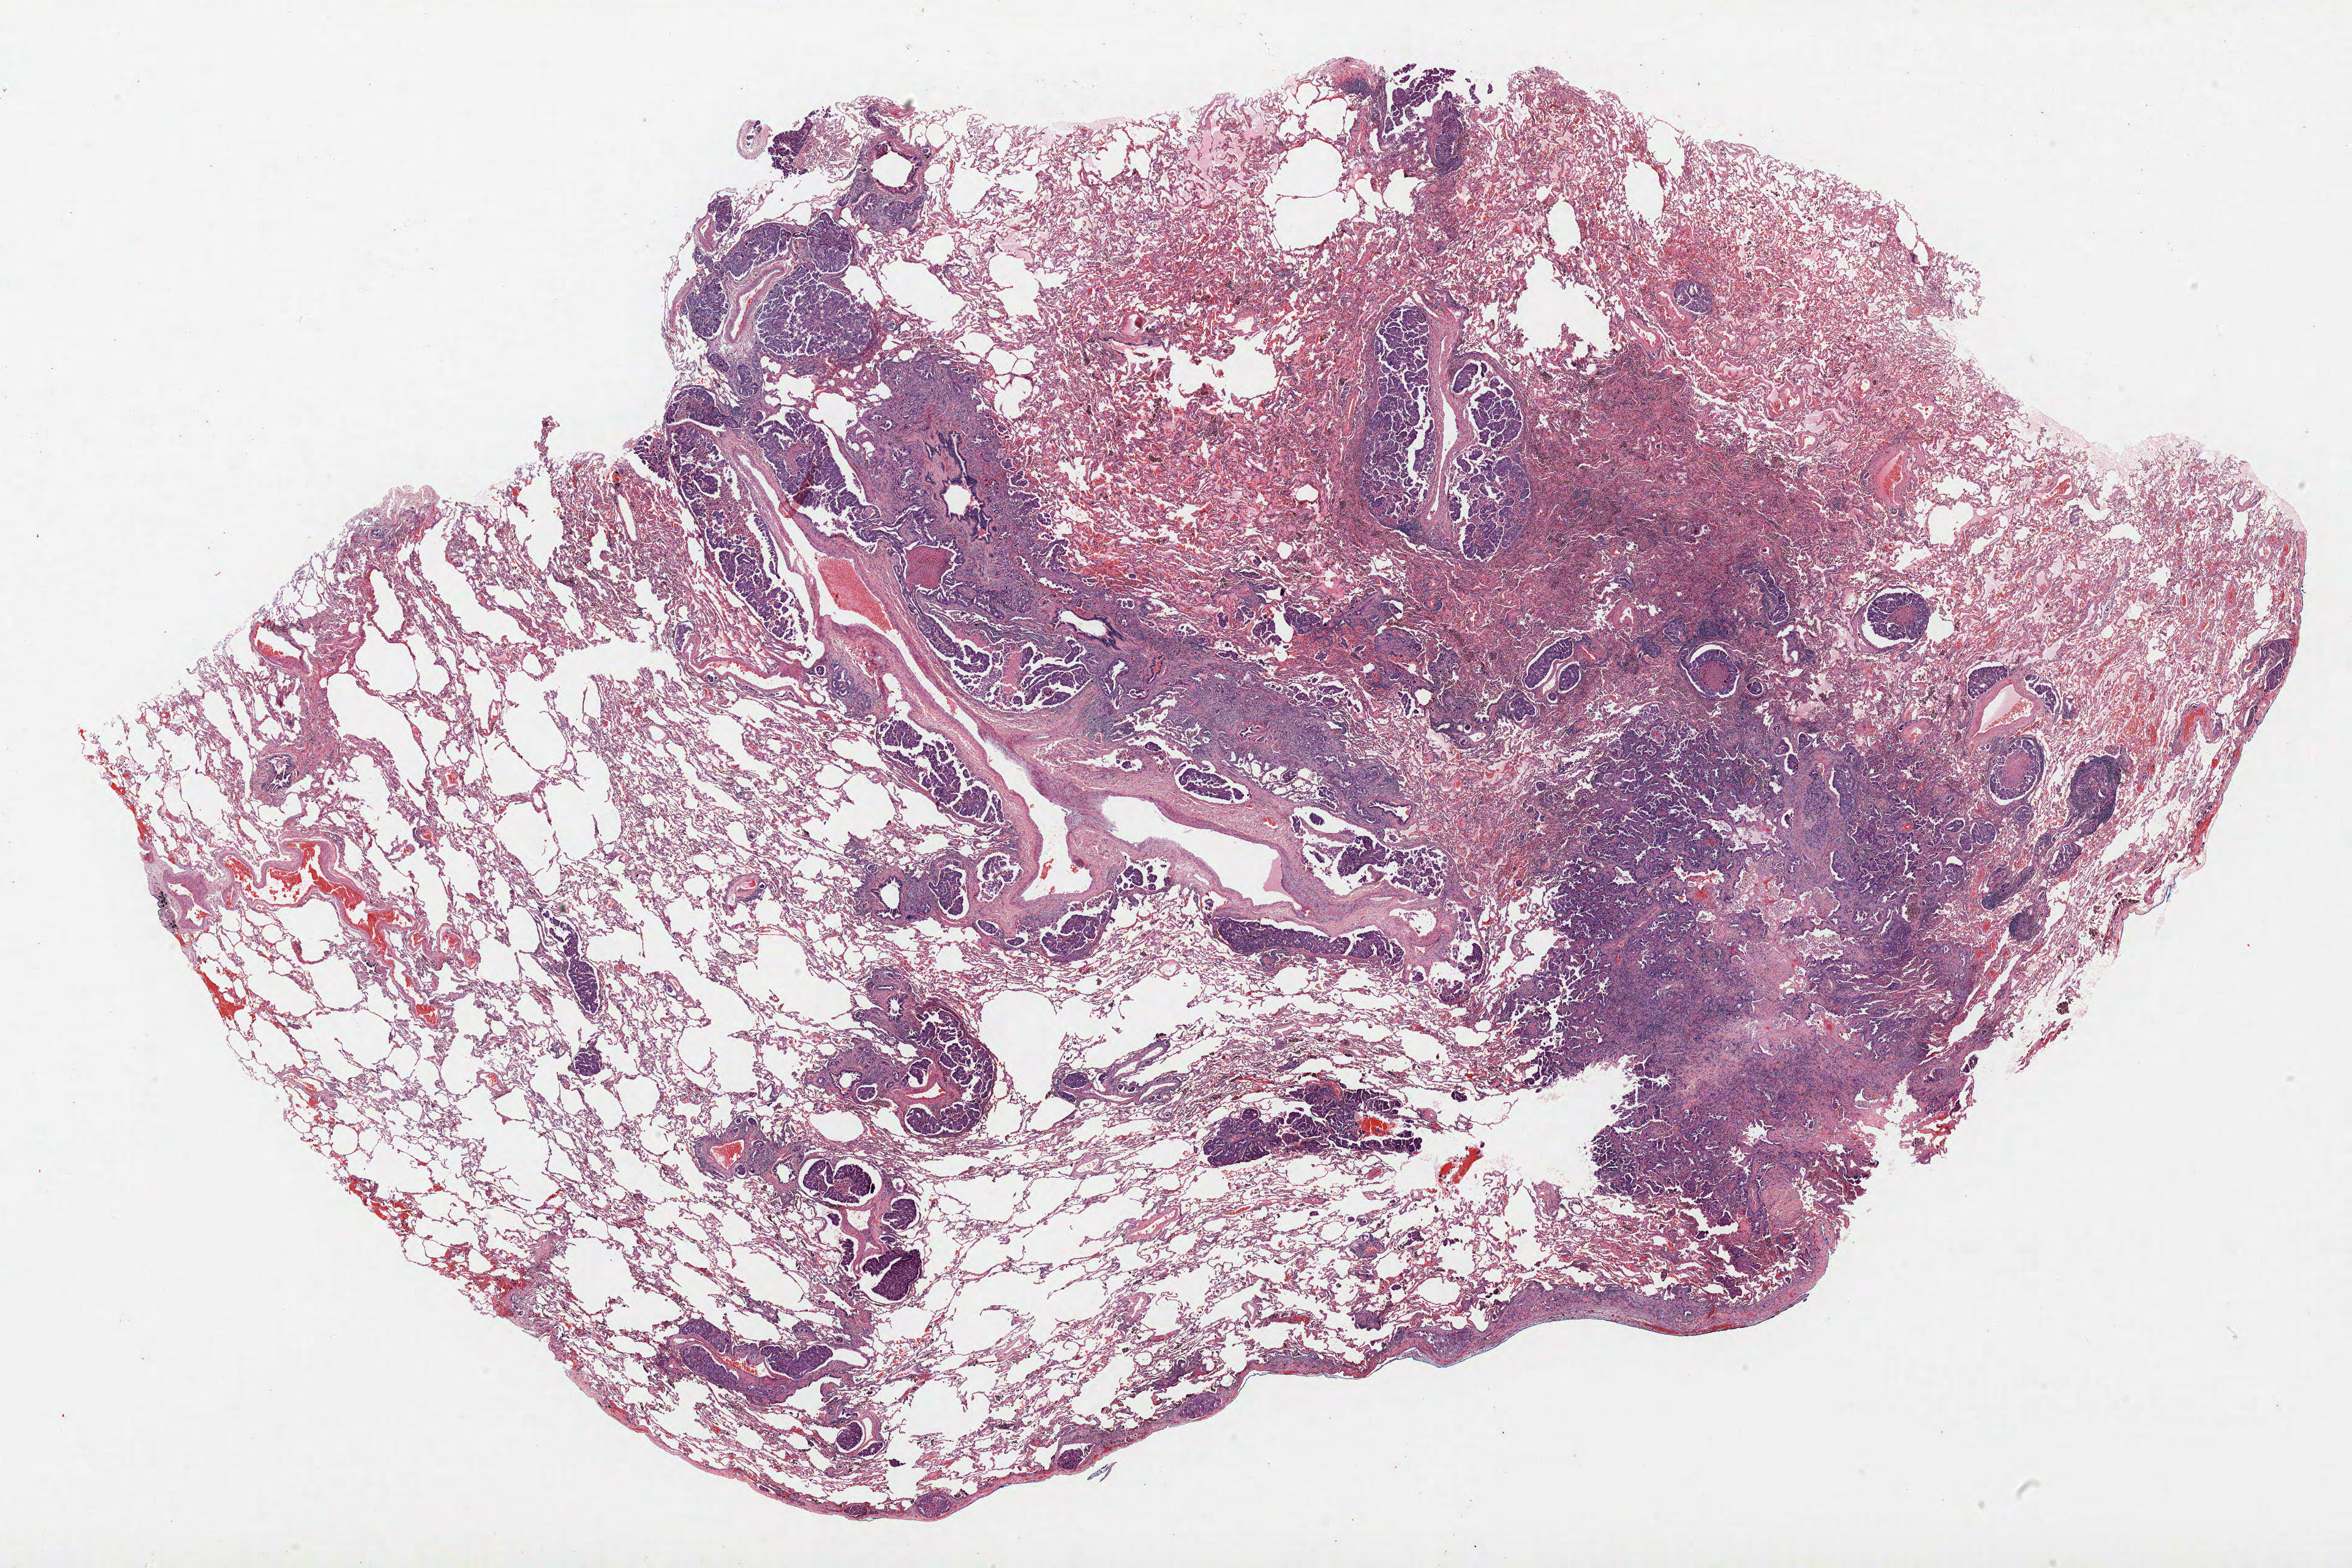
H&E-stained whole-slide image — a low-resolution overview of the entire scanned area, about 30.7 x 20.5 mm (from a 40x scan), formalin-fixed paraffin-embedded (FFPE) section, lung tissue. Male, age 60 at enrolment. Current smoker at enrolment. Grade: poorly differentiated (G3).
Primary tumour location (clinical record): left upper lobe. Stage (AJCC 6th edition): IIIA. Tumour size (pathology): 20 mm. Participant's lung-cancer diagnosis: Adenocarcinoma, NOS (ICD-O-3 8140/3).